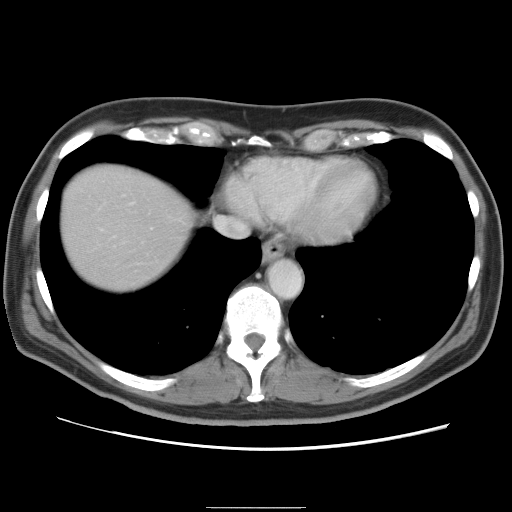
Contrast-enhanced abdominal CT, one axial slice; position 76 of 87 along the scan axis; 120 kVp; intravenous contrast given; soft-tissue window (W 400 / L 40 HU); 5 mm slice thickness; 512 × 512 image matrix. Male patient, age 63 years. Case-level facts recorded for this patient, not image findings: diagnosis: colorectal cancer liver metastases, imaged before liver resection; multiple liver metastases: no.
Annotated regions visible in this slice (expert manual segmentation):
- liver: bounding box [x1, y1, x2, y2] px = [60, 166, 192, 291]
- planned liver remnant (the part of the liver to remain after resection): [60, 180, 190, 291]